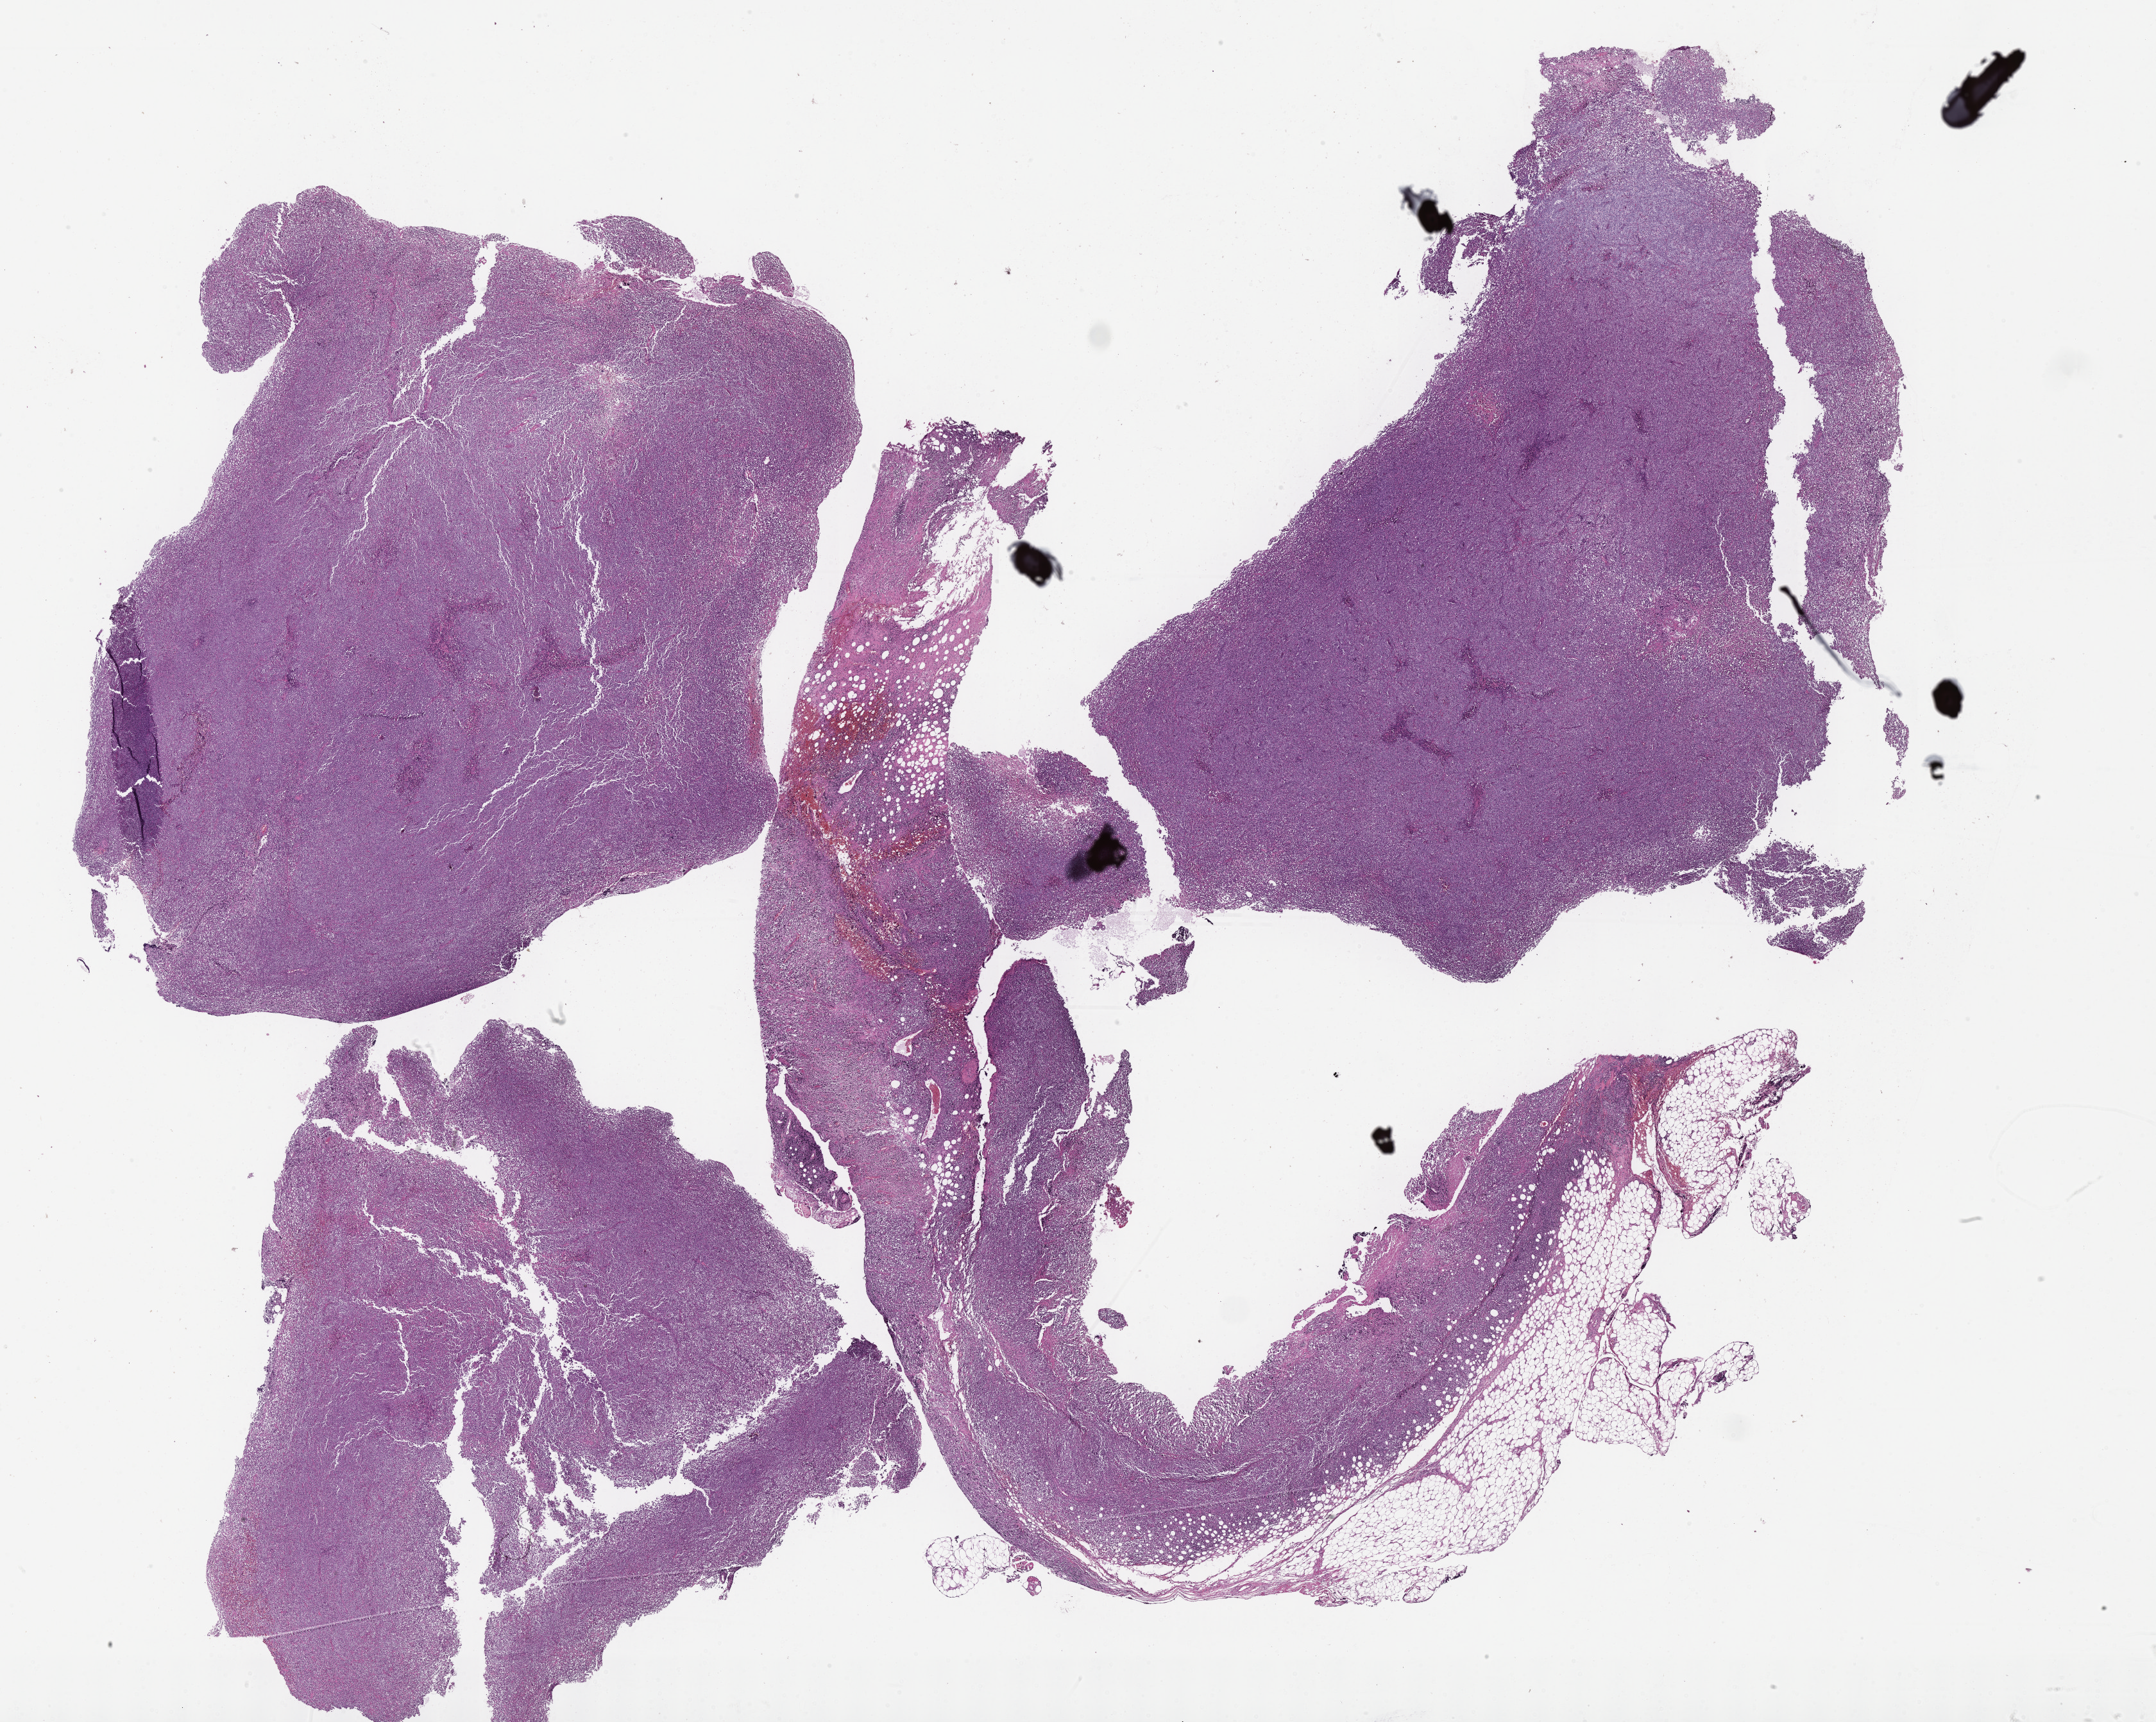
Whole-slide image, hematoxylin and eosin (H&E) stain, whole scanned area (about 27.2 x 21.7 mm) shown as a low-resolution overview. Female patient.
* specimen: tumor tissue